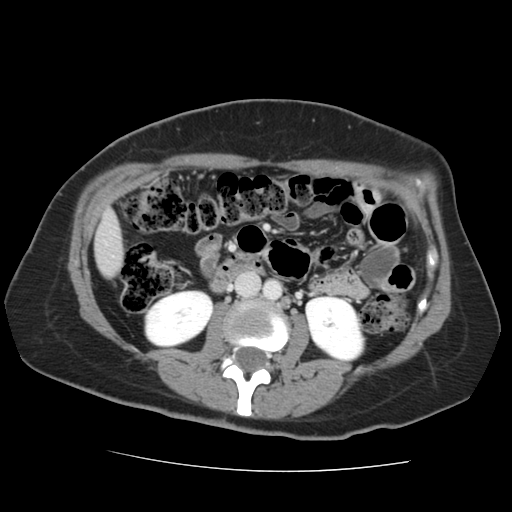
Contrast-enhanced abdominal CT, one axial slice. Intravenous contrast given. Soft-tissue window (W 400 / L 40 HU). 2.5 mm slice thickness. 512 × 512 image matrix, field of view 333 × 333 mm. Female patient, age 46 years. Case-level facts recorded for this patient, not image findings: diagnosis: colorectal cancer liver metastases, imaged before liver resection; multiple liver metastases: no; largest metastasis: 2.8 cm; chemotherapy before resection: yes.
Outlined on this slice (expert manual segmentation):
- liver: bounding box (x1, y1, x2, y2) in pixels: (95, 215, 124, 277)
- planned liver remnant (the part of the liver to remain after resection): (95, 215, 124, 269)